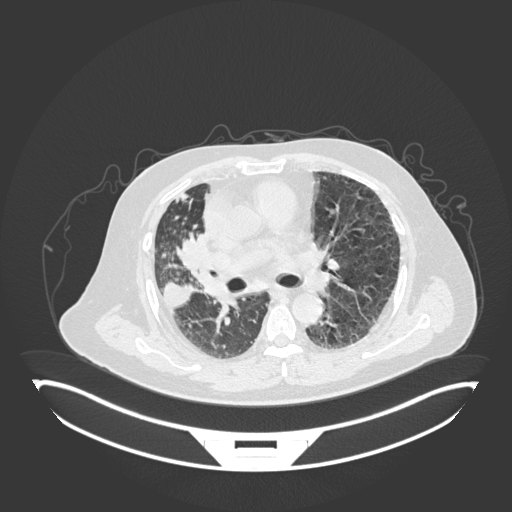
Chest CT, one axial slice. Position 90 of 201 along the scan axis. 120 kVp. Lung window (W 1500 / L -600 HU). 1 mm slice thickness. 512 × 512 image matrix, field of view 500 × 500 mm. Patient: male, 69 years. Case-level facts recorded for this patient, not image findings: clinical TNM (as recorded): T4 N3 M1.
Outlined on this slice (rectangle marked by the reading radiologist):
- lung tumour (recorded histology: adenocarcinoma): bounding box [x1, y1, x2, y2] px = [174, 228, 215, 278]